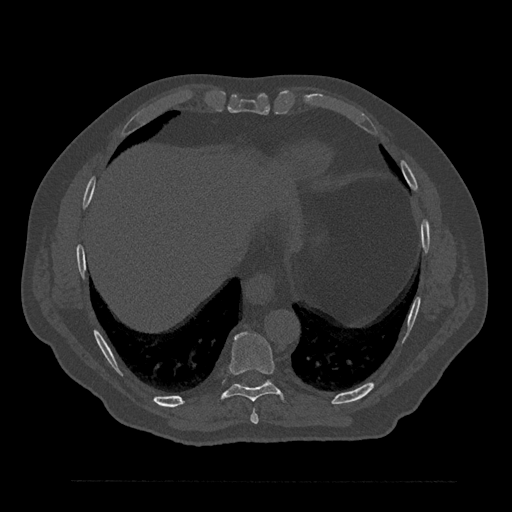
CT including the spine, one axial slice; slice 400 of 797 in the series (ordered by position); 120 kVp; bone window (W 1800 / L 400 HU); 0.5 mm slice thickness; 512 × 512 image matrix. Patient: male, 61 years. From the clinical record (not read from this slice): primary cancer: prostate.
Structures marked on this image (semi-automatically segmented with operator editing):
- T8 vertebra: box from (x=250, y=409) to (x=259, y=424) px
- T9 vertebra: (x=222, y=332)–(x=285, y=402)